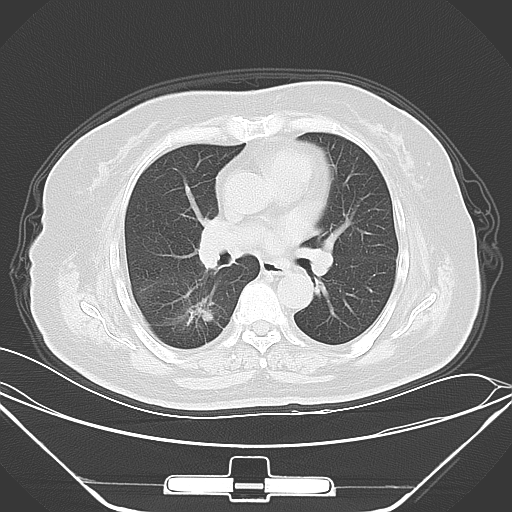
Chest CT, one axial slice; slice 35 of 64 in the series (ordered by position); lung window (W 1500 / L -600 HU); 5 mm slice thickness; 512 × 512 image matrix, field of view 396 × 396 mm. Patient: female, 70 years. From the clinical record (not read from this slice): clinical TNM (as recorded): T2 N0 M3.
Structures marked on this image (rectangle marked by the reading radiologist):
- lung tumour (recorded histology: adenocarcinoma): bounding box (x1, y1, x2, y2) in pixels: (170, 297, 235, 346)